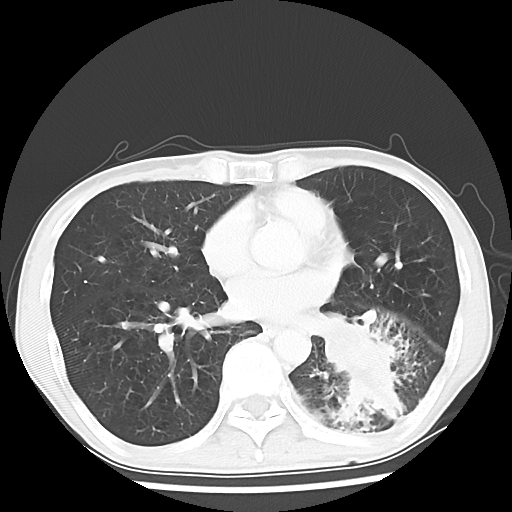
Chest CT, one axial slice; position 27 of 64 along the scan axis; reconstruction kernel LUNG; 120 kVp; lung window (W 1500 / L -600 HU); 5 mm slice thickness; 512 × 512 image matrix, field of view 313 × 313 mm. Patient: male, 68 years. From the clinical record (not read from this slice): clinical TNM (as recorded): T4 N0 M0.
Outlined on this slice (rectangle marked by the reading radiologist):
- lung tumour (recorded histology: squamous cell carcinoma): bounding box [x1, y1, x2, y2] px = [313, 309, 410, 441]